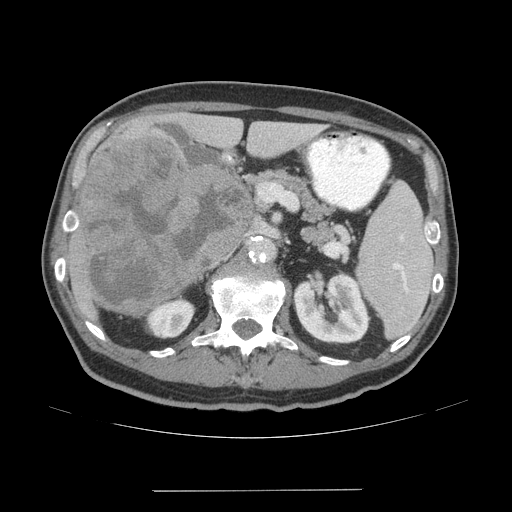
Contrast-enhanced abdominal CT (liver protocol), one axial slice; position 25 of 77 along the scan axis; reconstruction kernel STANDARD; soft-tissue window (W 400 / L 40 HU); 2.5 mm slice thickness; 512 × 512 image matrix, field of view 400 × 400 mm. Case-level facts recorded for this patient, not image findings: diagnosis: hepatocellular carcinoma (patient treated with transarterial chemoembolisation; whether this scan precedes or follows treatment is not stated here); TNM stage (as recorded): Stage-IVA; Child-Pugh class: A; tumour nodularity: uninodular.
Annotated regions visible in this slice (semi-automatic segmentation, software-assisted and operator-edited):
- liver parenchyma outside the tumour (the mass and vessels are separate outlines, so this box may not span the whole liver): bounding box (x1, y1, x2, y2) in pixels: (66, 112, 320, 314)
- mass: (78, 138, 255, 318)